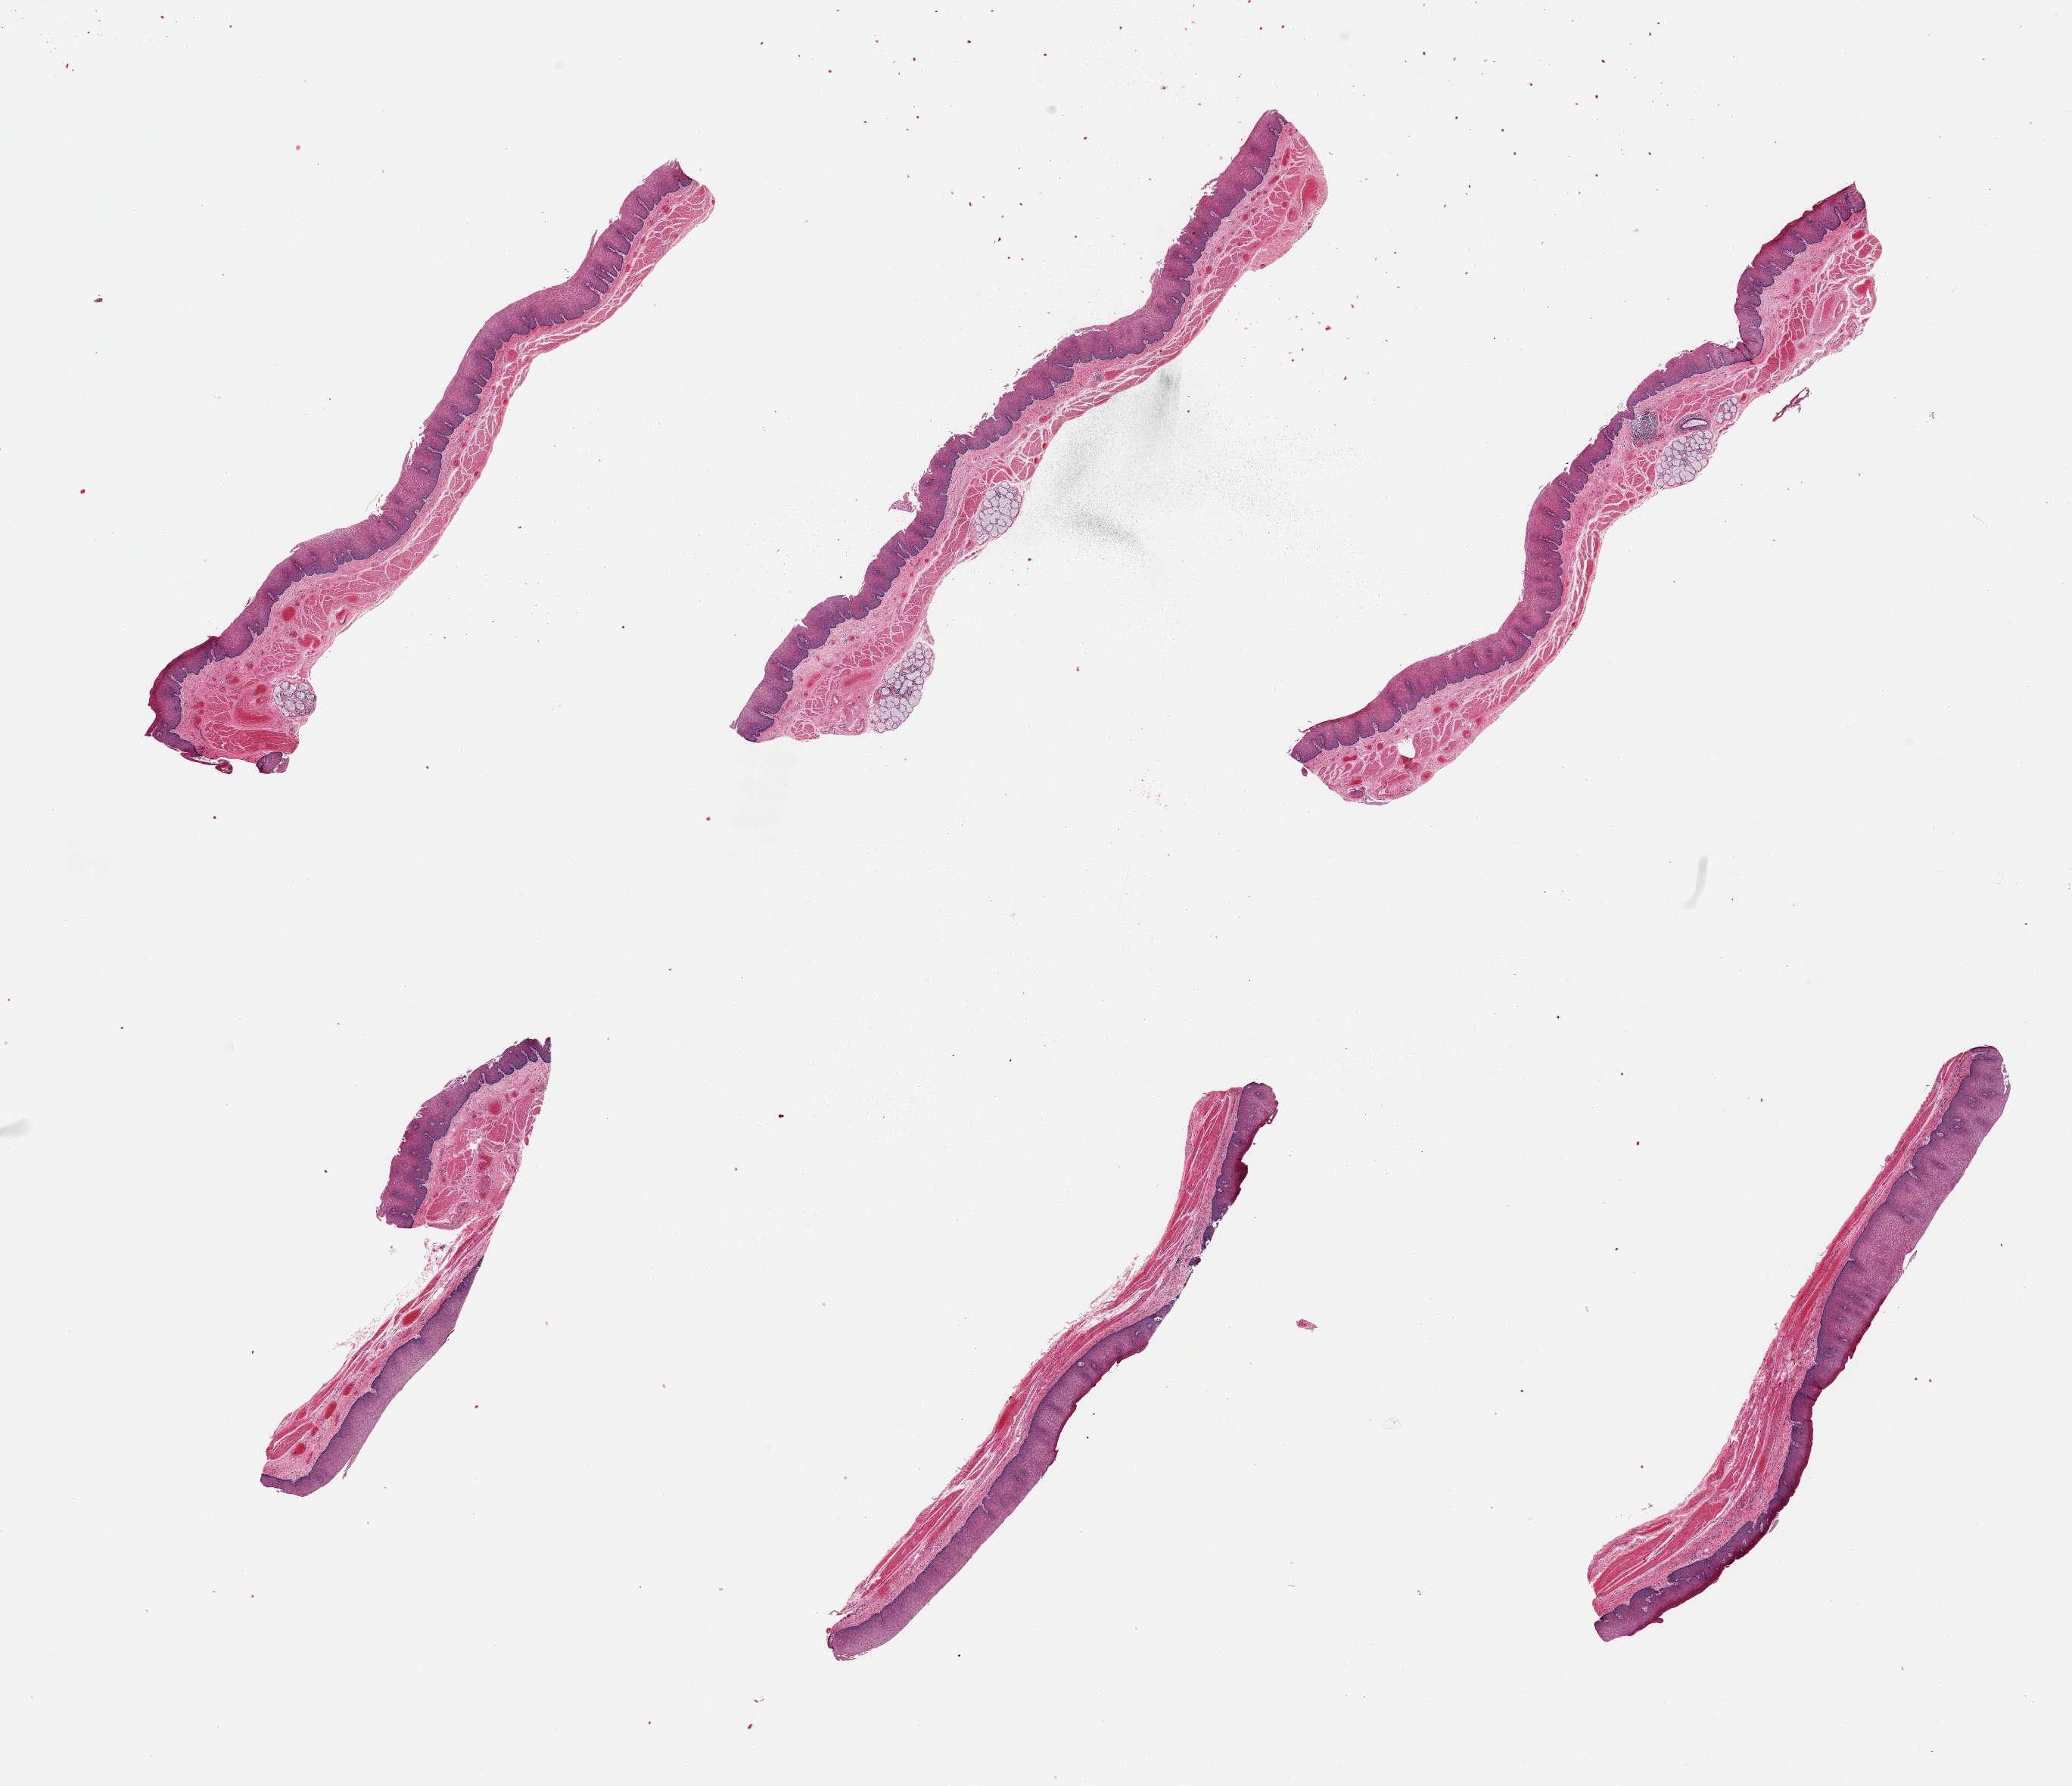
Hematoxylin and eosin (H&E) whole-slide image, brightfield, a low-resolution overview of the entire scanned area, about 21.7 x 18.7 mm (acquisition: 20x scan); PAXgene-fixed paraffin-embedded (PFPE) section; target tissue: esophageal mucous membrane; tissue donor sample.
Pathologist's review note for this sample: 6 pieces squamous mucosa is ~0.3mm, 20-50% thickness; incidental submucosal mucus glands present.